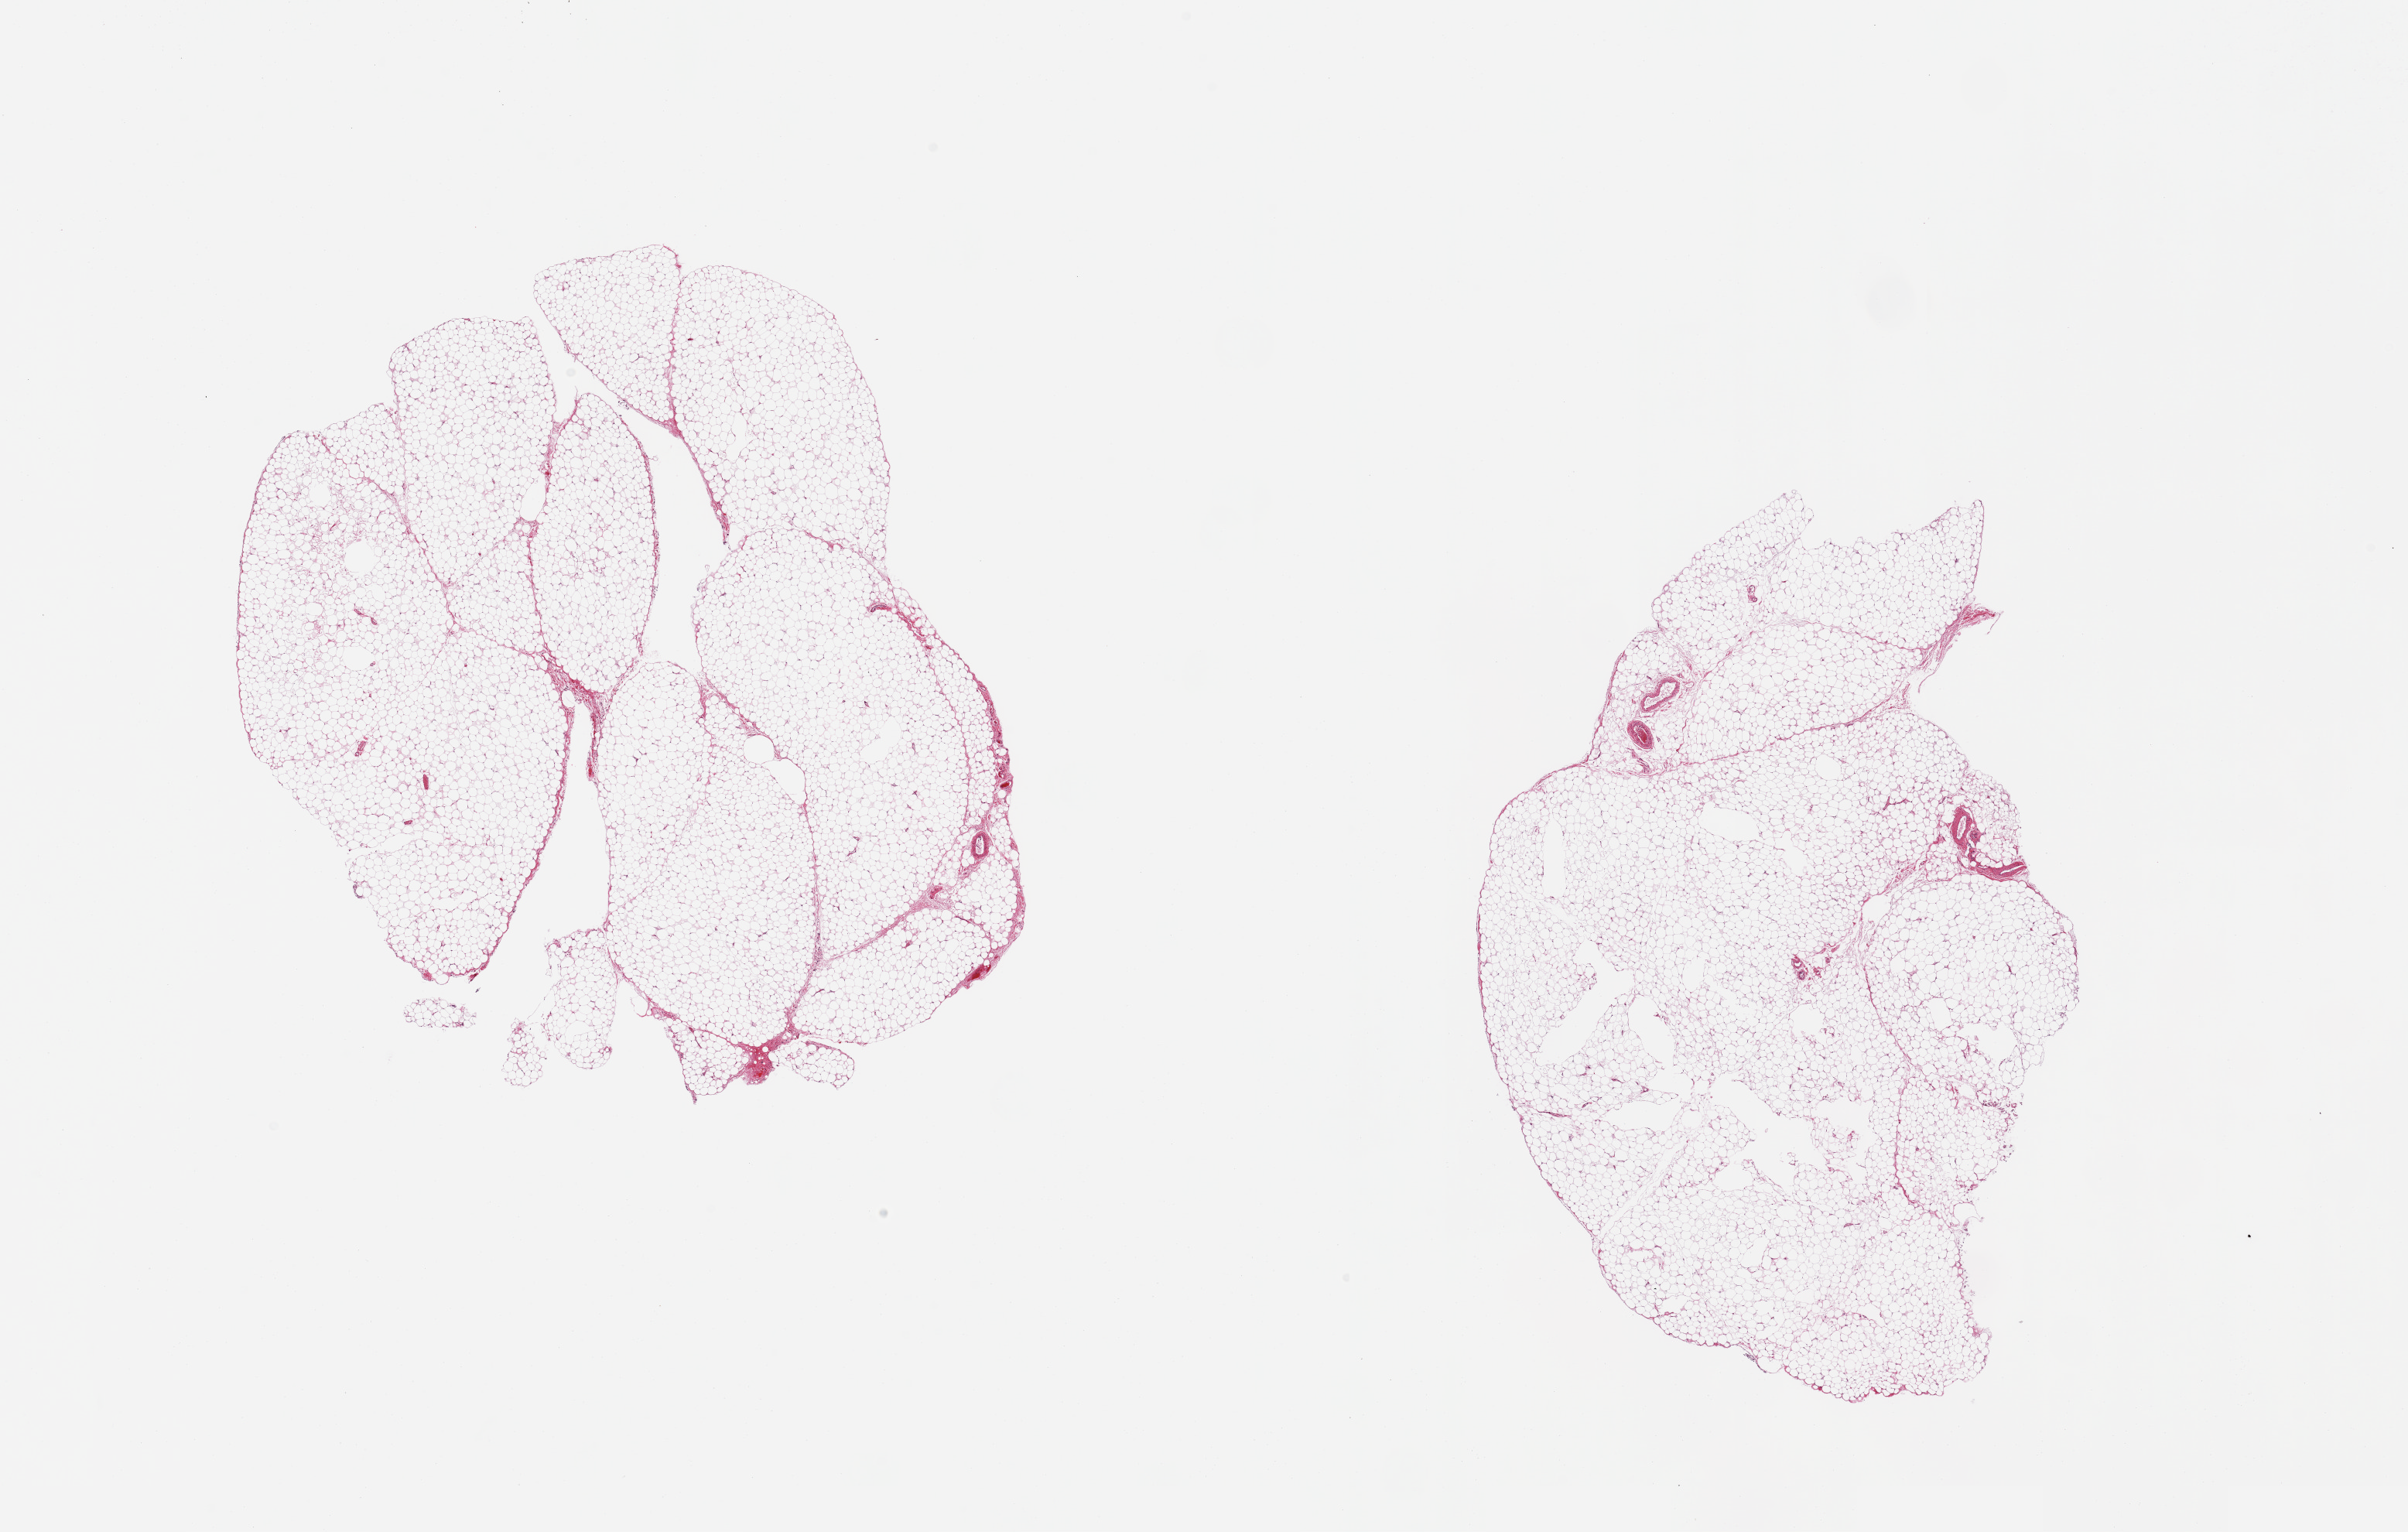
Whole-slide image, H&E stain, whole scanned area (about 24.6 x 15.7 mm, slide scanned at 20x) shown as a low-resolution overview, PAXgene-fixed, paraffin-embedded tissue, section of omentum (target tissue), tissue donor sample. Male donor.
- reviewer comment on this tissue sample: 2 pieces; ~5% vascular/mesothelial/fascia elements